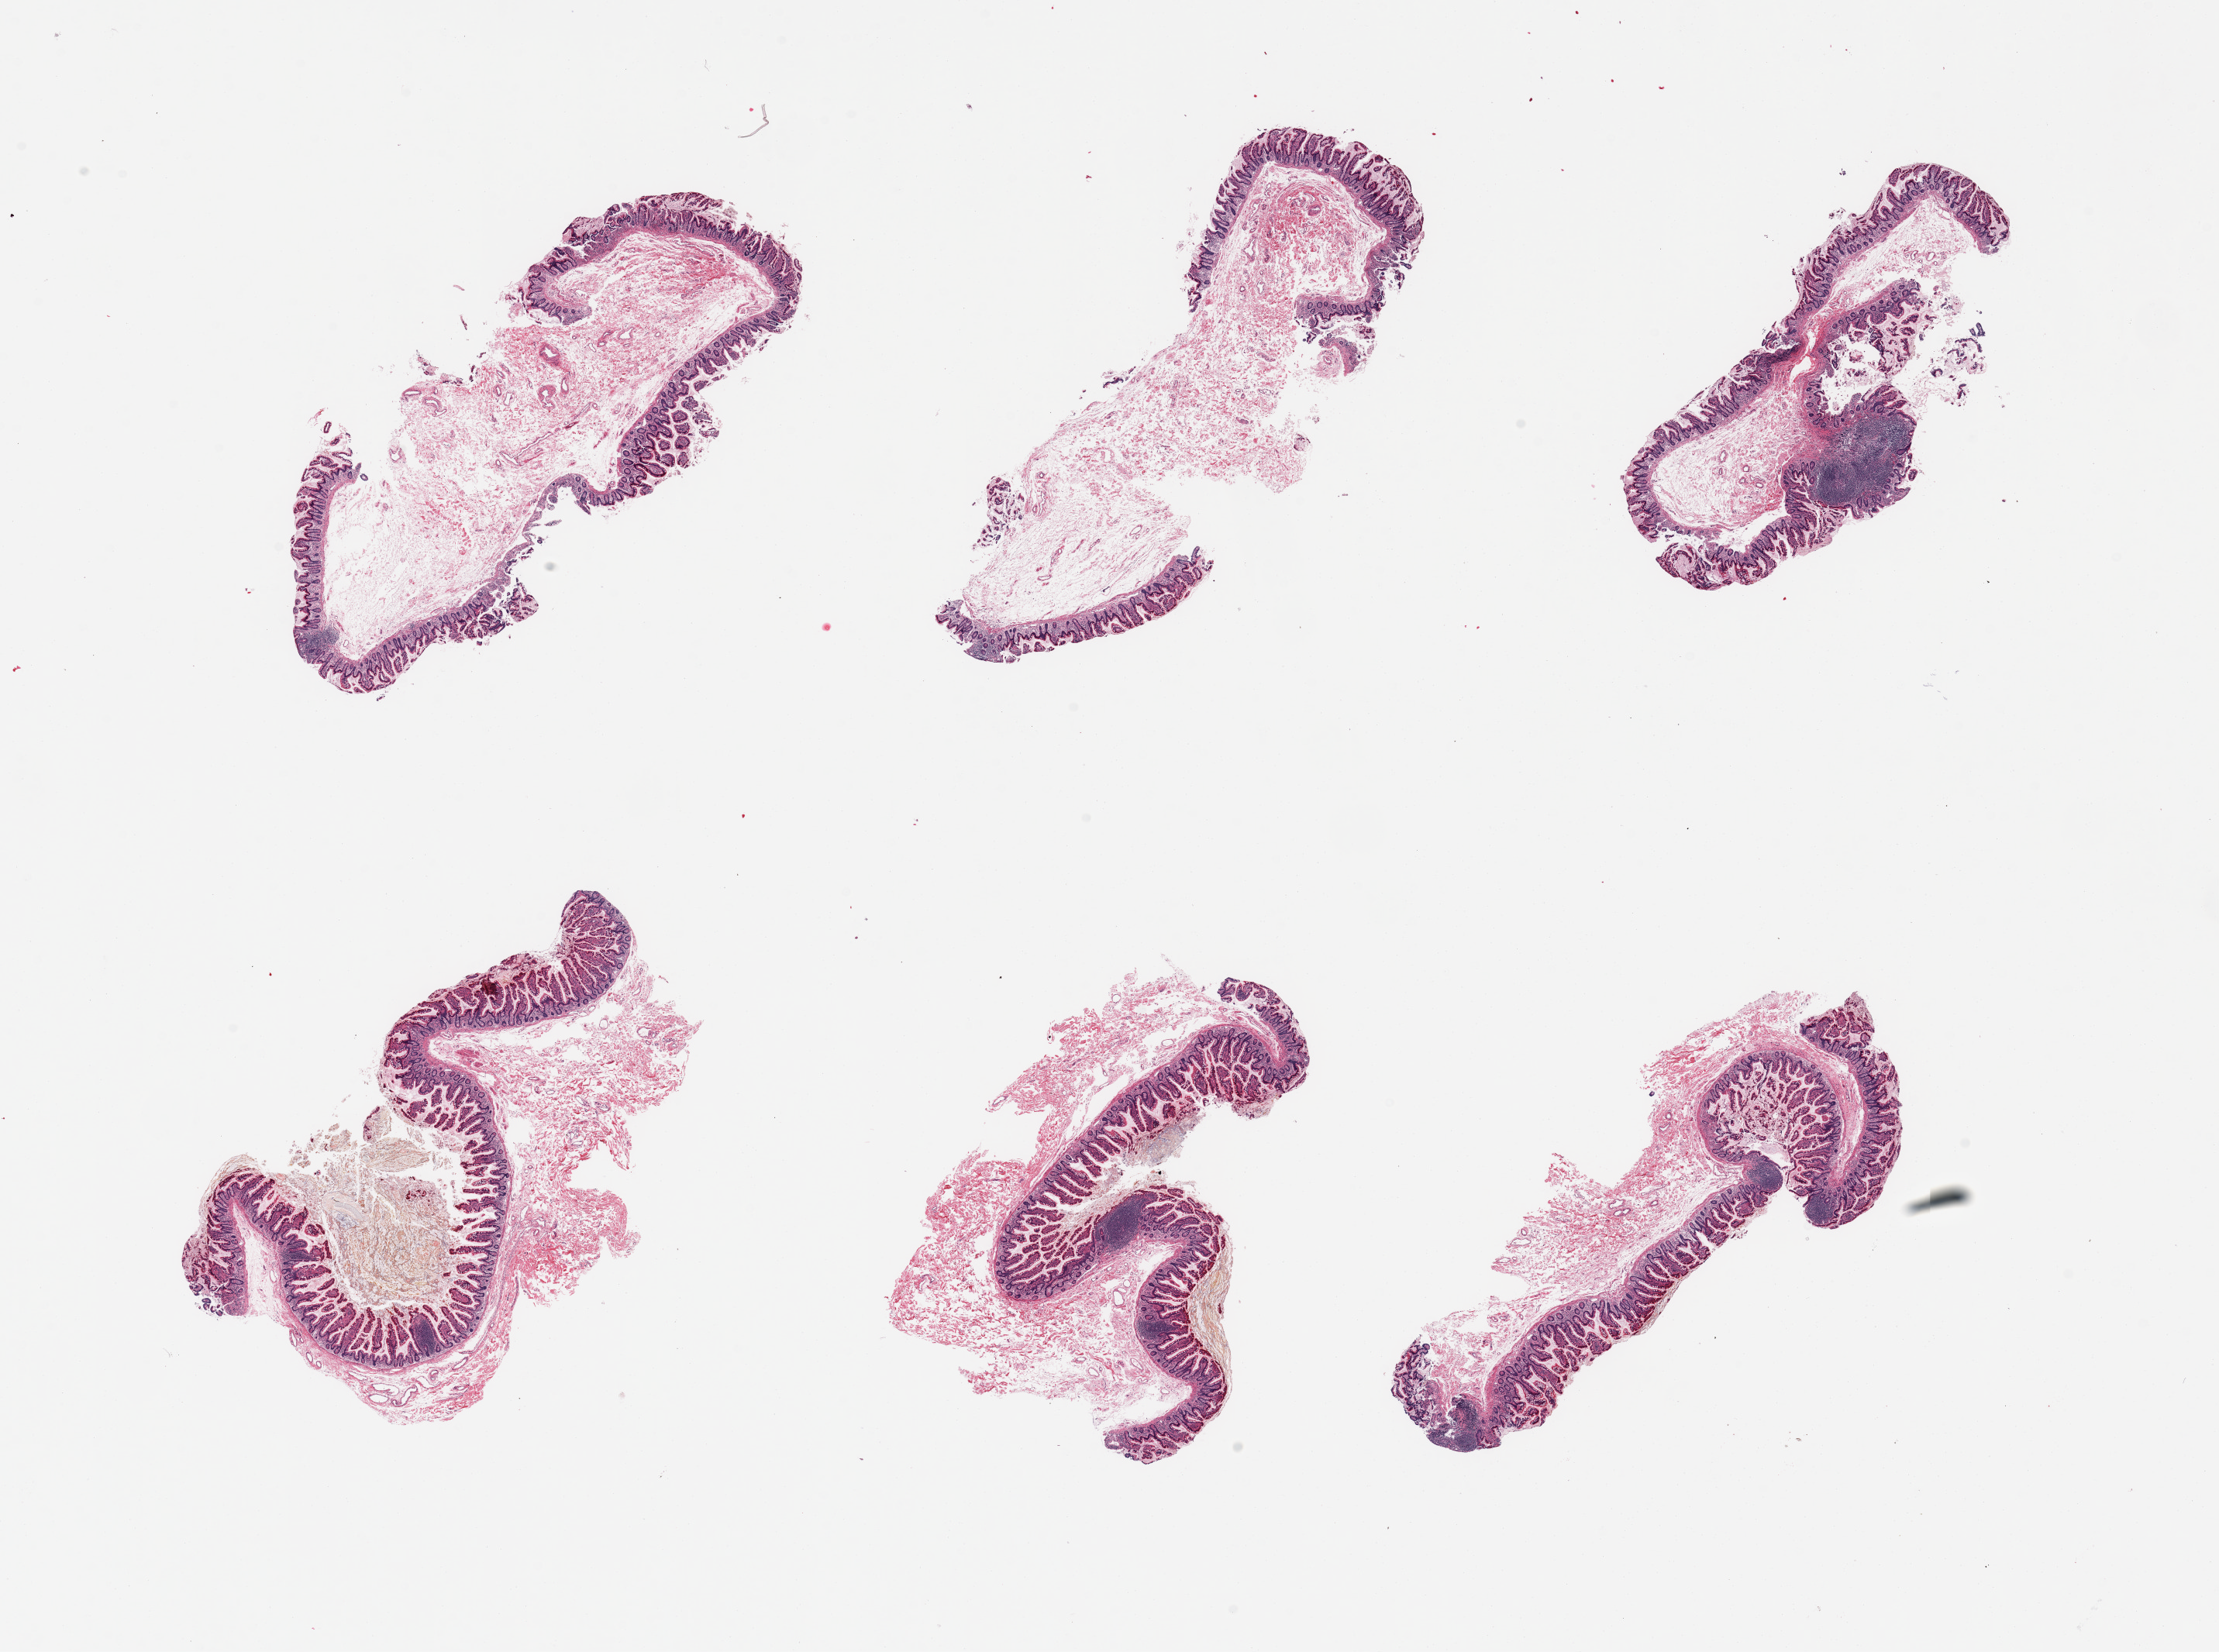
Digitized H&E-stained section — shown as a low-resolution overview of the whole scanned area (about 22.6 x 16.9 mm), PAXgene-fixed, paraffin-embedded tissue, sampled site (target tissue): ileum, tissue donor sample. Donor: male.
Review note (as recorded): 6 pieces; well preserved mucosa/submucosa with scattered lymphoid tissue, insufficient for analysis.